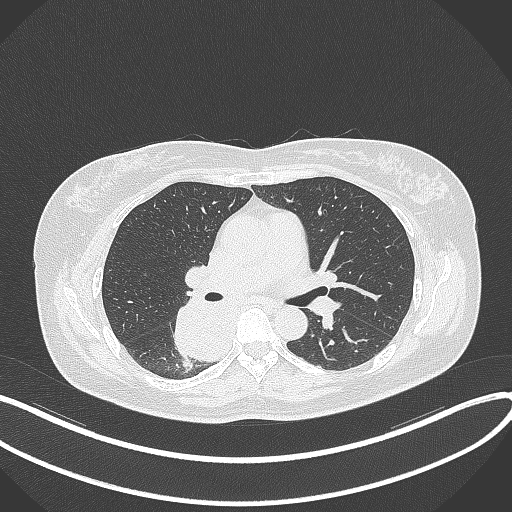
Chest CT, one axial slice. Slice 210 of 331 in the series (ordered by position). 120 kVp. Lung window (W 1500 / L -600 HU). 1 mm slice thickness. 512 × 512 image matrix, field of view 400 × 400 mm. Patient: female, 54 years. Case-level facts recorded for this patient, not image findings: clinical TNM (as recorded): T4 N0 M0.
Structures marked on this image (bounding box drawn by a radiologist):
- lung tumour (recorded histology: adenocarcinoma): box from (x=173, y=294) to (x=230, y=366) px